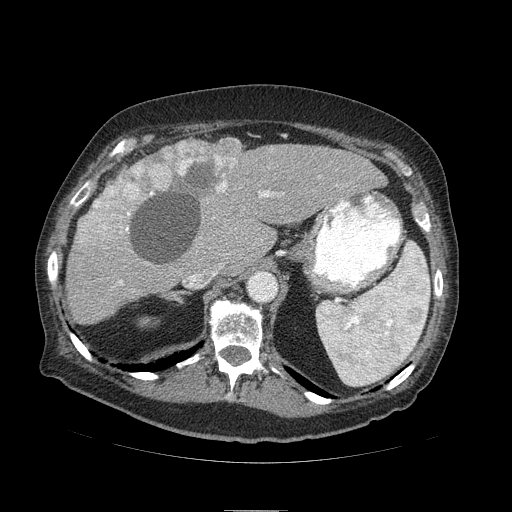
Contrast-enhanced abdominal CT (liver protocol), one axial slice; slice 65 of 103 in the series (ordered by position); soft-tissue window (W 400 / L 40 HU); 2.5 mm slice thickness; 512 × 512 image matrix, field of view 440 × 440 mm. From the clinical record (not read from this slice): diagnosis: hepatocellular carcinoma (patient treated with transarterial chemoembolisation; whether this scan precedes or follows treatment is not stated here); TNM stage (as recorded): Stage-IIIA; Child-Pugh class: B; tumour differentiation: well differentiated; tumour nodularity: multinodular.
Structures marked on this image (semi-automatic segmentation, software-assisted and operator-edited):
- liver parenchyma outside the tumour (the mass and vessels are separate outlines, so this box may not span the whole liver): bounding box <66,138,386,324> (left, top, right, bottom; pixels)
- mass: <78,137,240,250>
- liver vessels: <213,192,269,275>